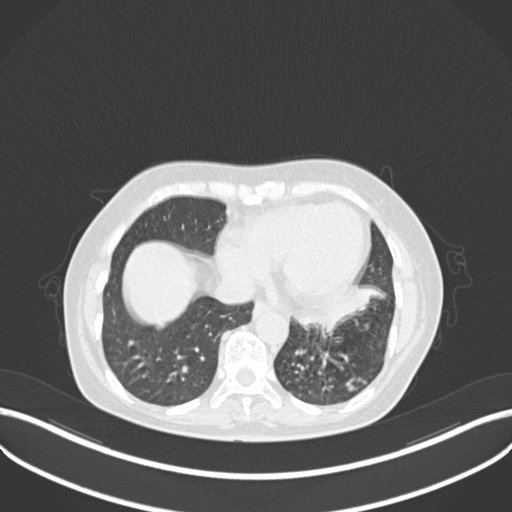
Chest CT, one axial slice; position 79 of 270 along the scan axis; reconstruction kernel B30f; 120 kVp; lung window (W 1500 / L -600 HU); 1 mm slice thickness; 512 × 512 image matrix, field of view 400 × 400 mm. Female patient, age 63 years. From the clinical record (not read from this slice): clinical TNM (as recorded): T1b N0 M0; histopathological grade: G2-3.
Structures marked on this image (bounding box drawn by a radiologist):
- lung tumour (recorded histology: adenocarcinoma): box from (x=293, y=284) to (x=388, y=336) px